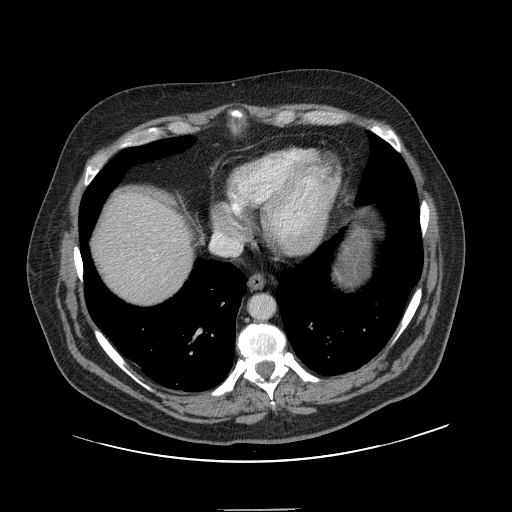
Contrast-enhanced abdominal CT, one axial slice; soft-tissue window (W 400 / L 40 HU); 2.5 mm slice thickness; 512 × 512 image matrix. Male patient, age 61 years. Case-level facts recorded for this patient, not image findings: diagnosis: colorectal cancer liver metastases, imaged before liver resection; multiple liver metastases: yes.
Annotated regions visible in this slice (expert manual segmentation):
- liver: bounding box <94,192,192,305> (left, top, right, bottom; pixels)
- planned liver remnant (the part of the liver to remain after resection): <94,192,193,304>